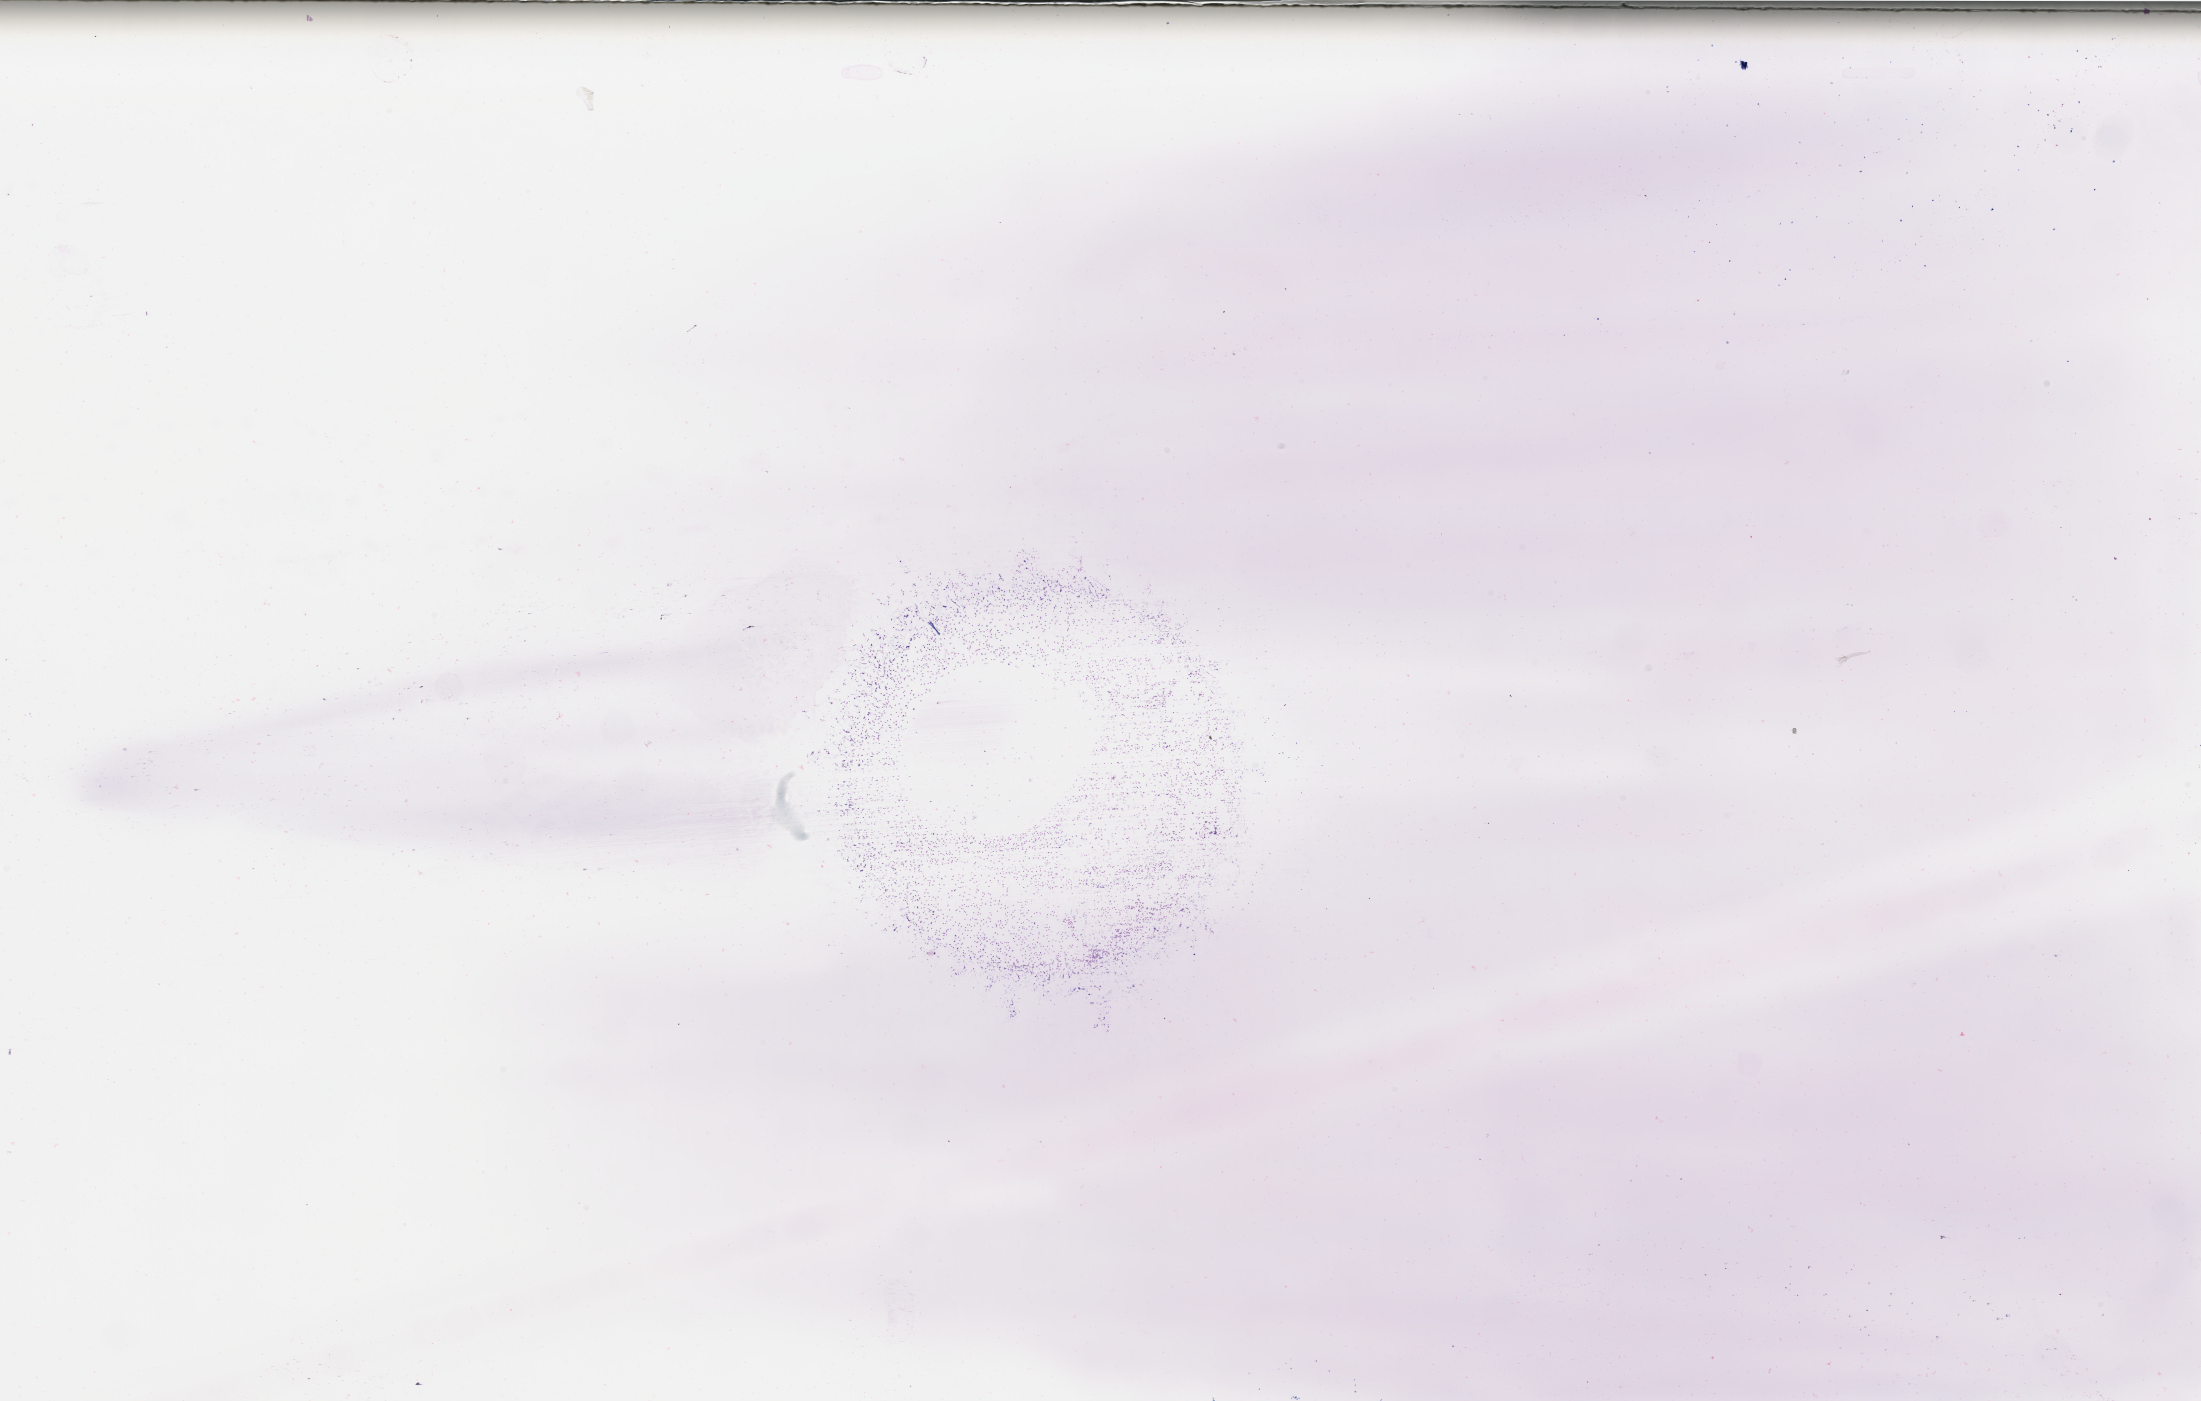
H&E-stained whole-slide image — low-resolution overview of the scanned area, about 34.8 x 22.1 mm. Peripheral blood (leukaemic) sample. 69-year-old female patient. Blasts: 75%.
WHO classification: AML not otherwise specified. Diagnosis: Acute Myeloid Leukemia.